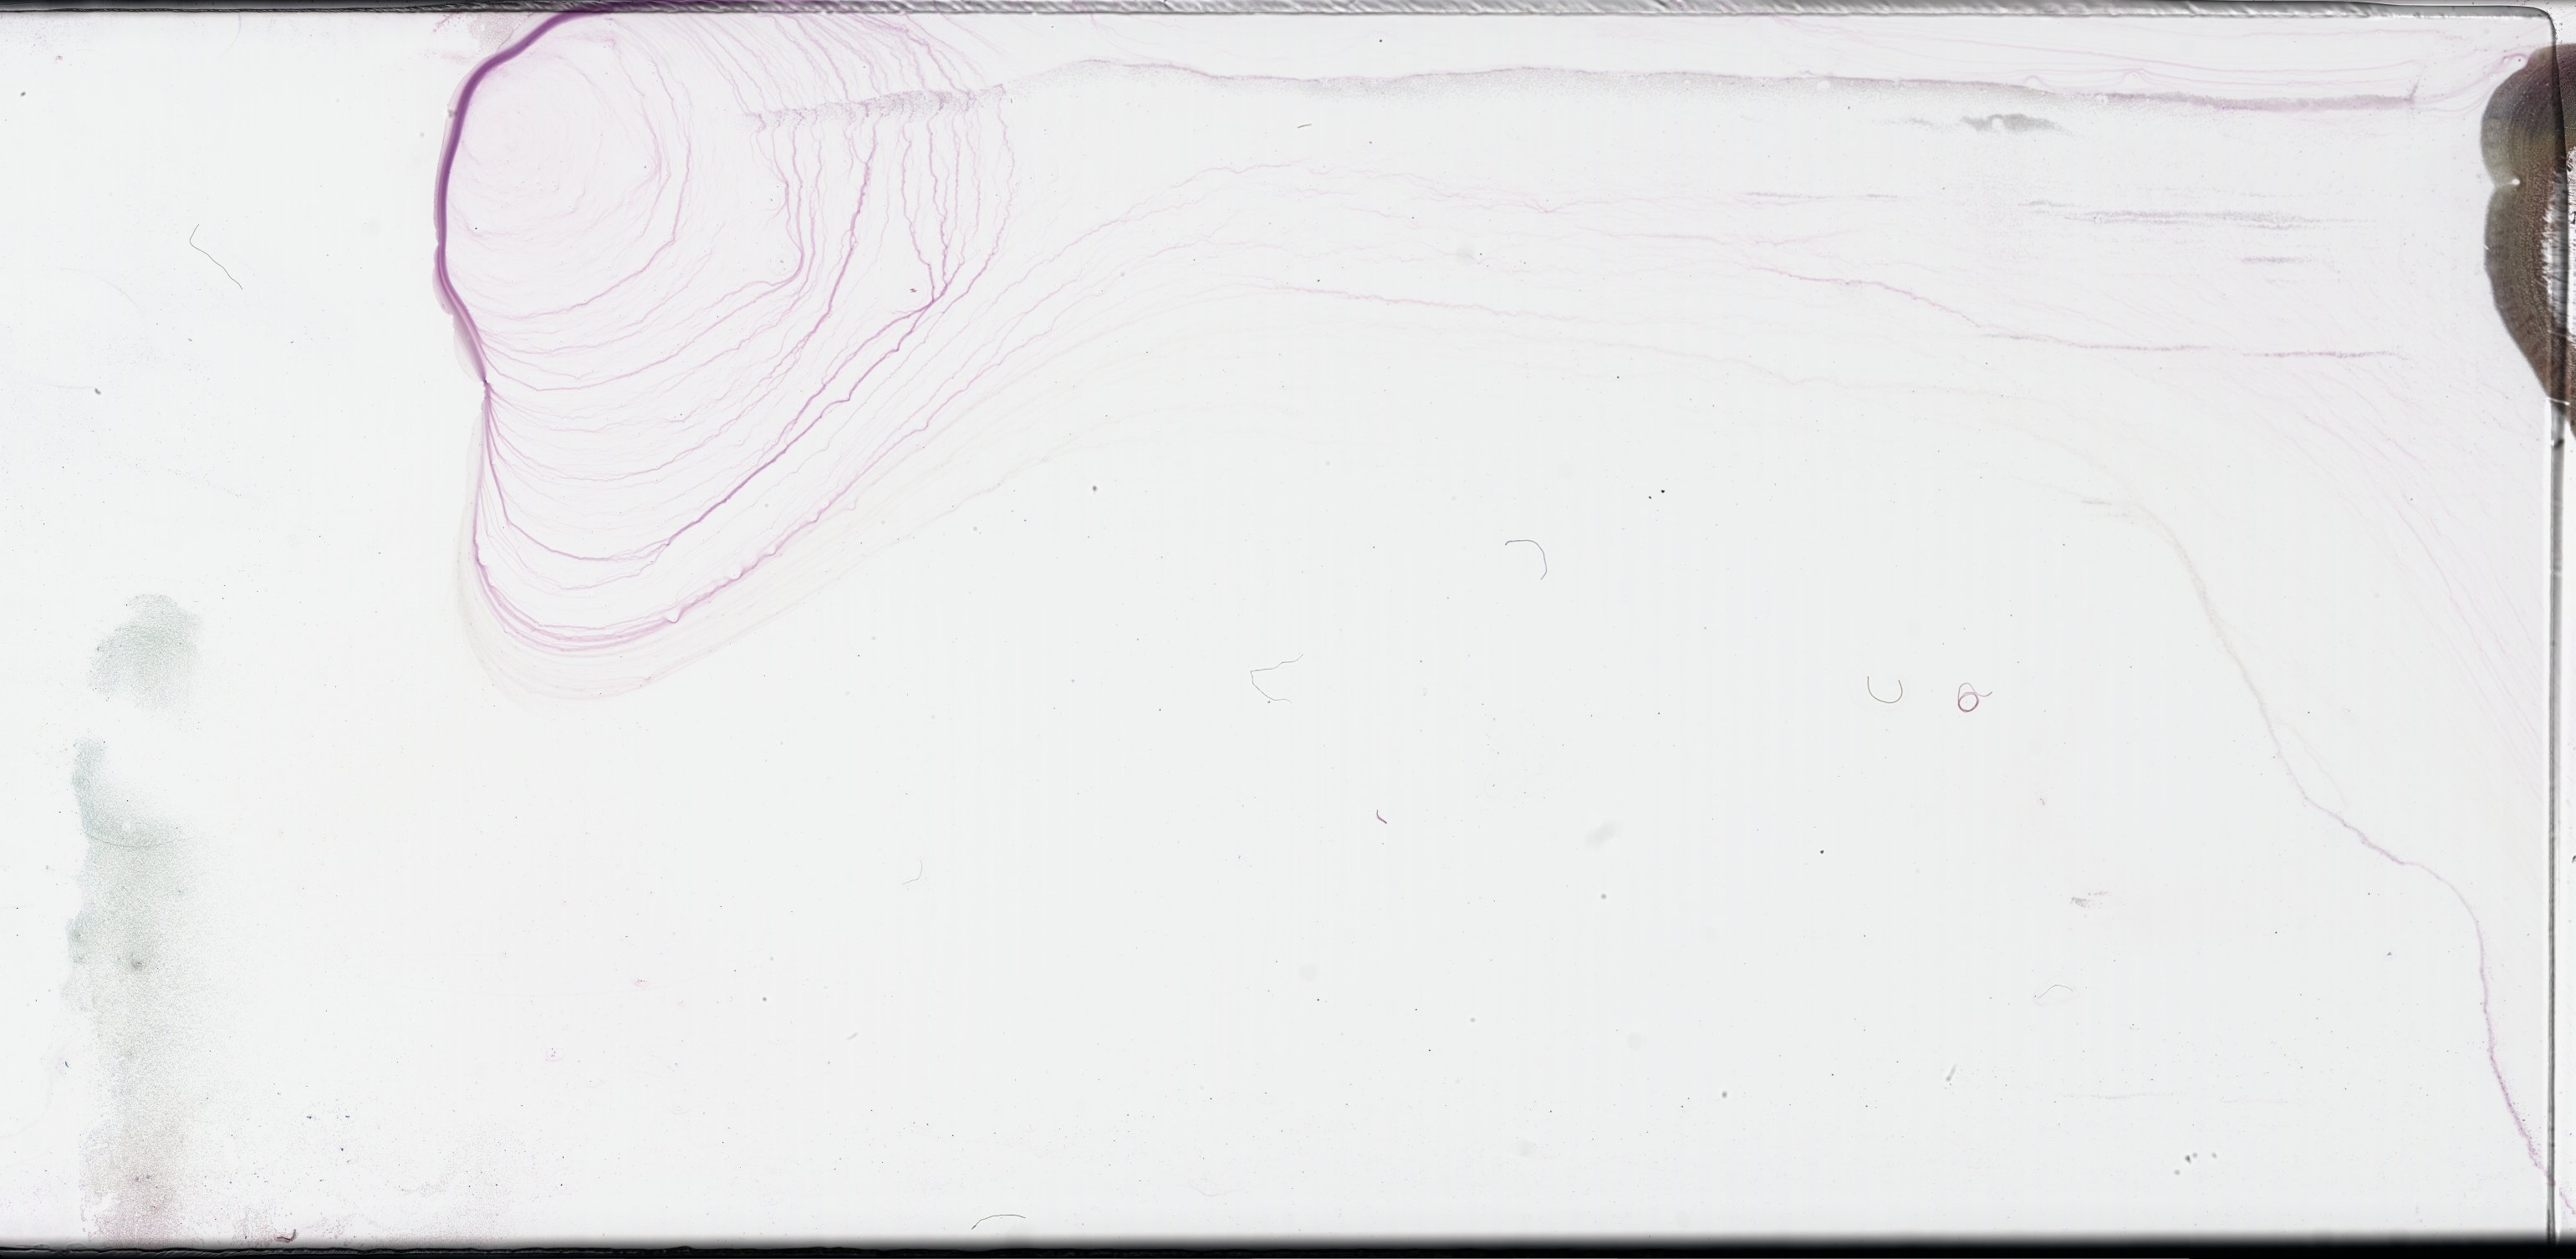
Whole-slide image of a bone marrow smear, Wright–Giemsa stain, low-resolution overview of the scanned area, about 49.8 x 24.3 mm; specimen time point: collected at baseline (before treatment). Patient sex: male.
From a patient with: Plasma Cell Myeloma.